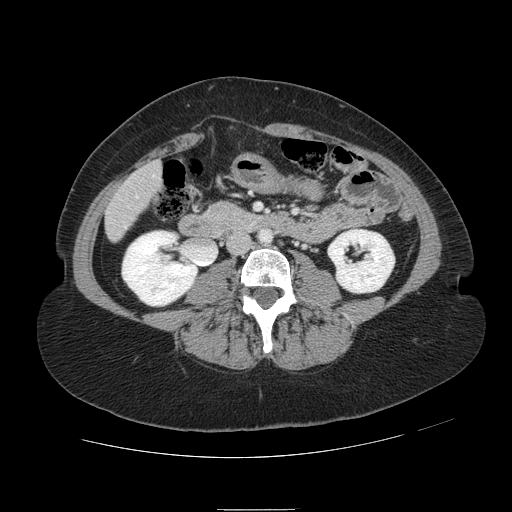
Contrast-enhanced abdominal CT, one axial slice; slice 12 of 121 in the series (ordered by position); 120 kVp; intravenous contrast given; soft-tissue window (W 400 / L 40 HU); 2.5 mm slice thickness; 512 × 512 image matrix, field of view 400 × 400 mm. Female patient, age 52 years. Case-level facts recorded for this patient, not image findings: diagnosis: colorectal cancer liver metastases, imaged before liver resection; multiple liver metastases: yes; largest metastasis: 6.3 cm; disease in both lobes: no.
Annotated regions visible in this slice (outlined manually by an expert reader):
- hepatic veins: bounding box [x1, y1, x2, y2] px = [136, 175, 155, 198]
- liver: [106, 164, 162, 240]